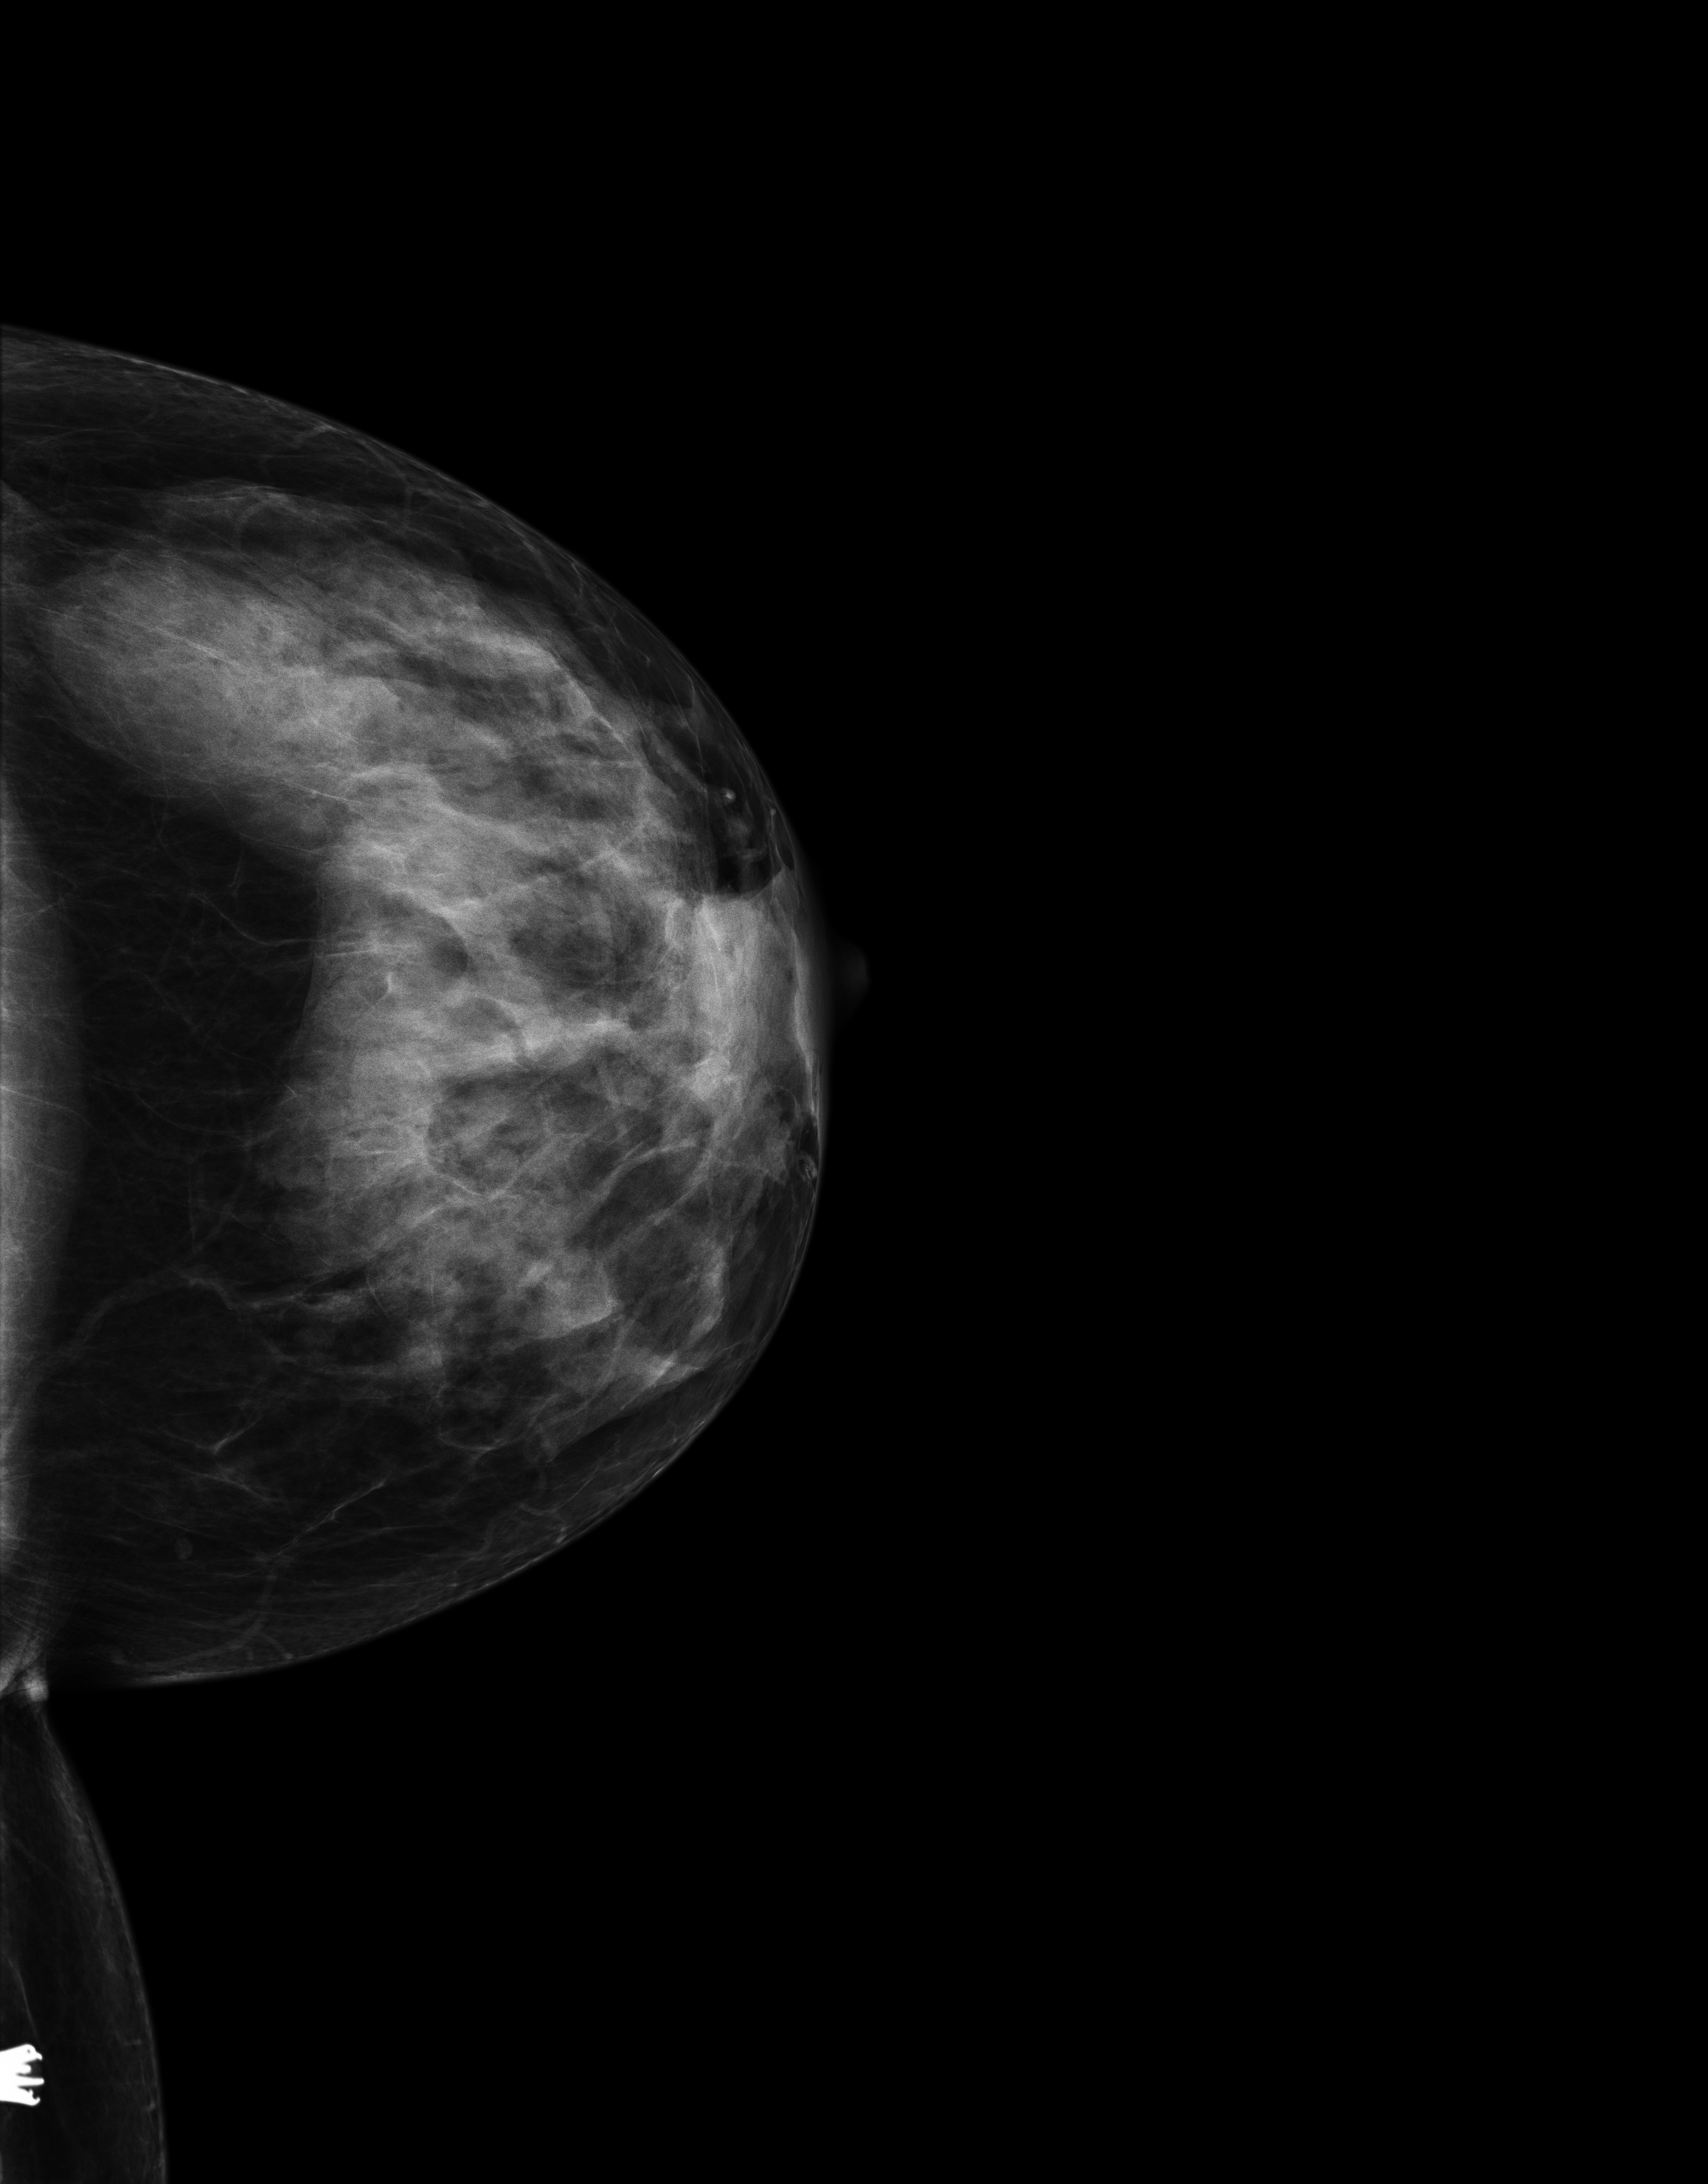
Annual screening mammography examination; compressed breast thickness 50 mm; system: Senographe Essential ADS_56.21.3. Female patient, age 61 years.
Image type: full-field digital mammogram. Breast: left. Projection: CC view.